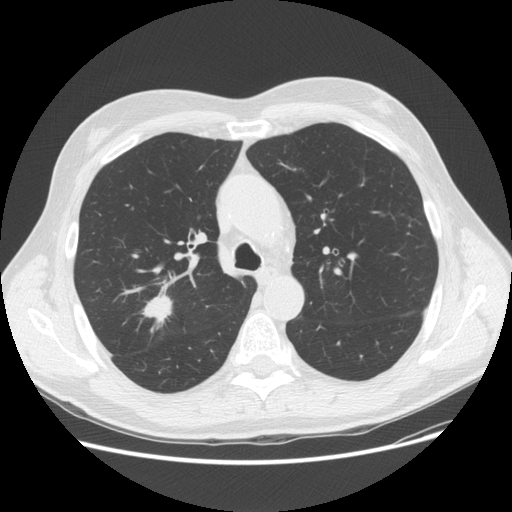
Low-dose screening chest CT, one axial slice; slice 106 of 156 in the series (ordered by position); reconstruction kernel STANDARD; 120 kVp; lung window (W 1500 / L -600 HU); 512 × 512 image matrix, field of view 380 × 380 mm.
Structures marked on this image (outlined manually by an expert reader):
- lesion 1 (tumor, upper lobe of right lung): bounding box [x1, y1, x2, y2] px = [141, 292, 173, 333]